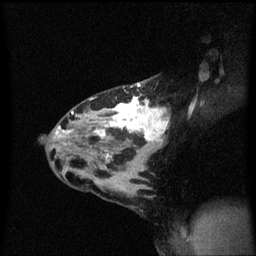
Breast MRI (dynamic contrast-enhanced), one sagittal slice. Slice 37 of 60 in the series (ordered by position). Dynamic contrast-enhanced series, image 2 of 3 at this slice position (ordered by acquisition). 1.5 T. TE 4.2 ms, TR 8.4 ms. 2 mm slice thickness. 256 × 256 image matrix, field of view 200 × 200 mm. Patient: female, 32 years.
Annotated regions visible in this slice (semi-automatic segmentation, software-assisted and operator-edited):
- analysis volume of interest (the breast-tissue region the enhancement analysis was run in; not a lesion): bounding box <55,78,170,167> (left, top, right, bottom; pixels)
- tumour enhancement mask (voxels above the 70 % enhancement threshold inside the analysis volume of interest): <57,82,170,161>